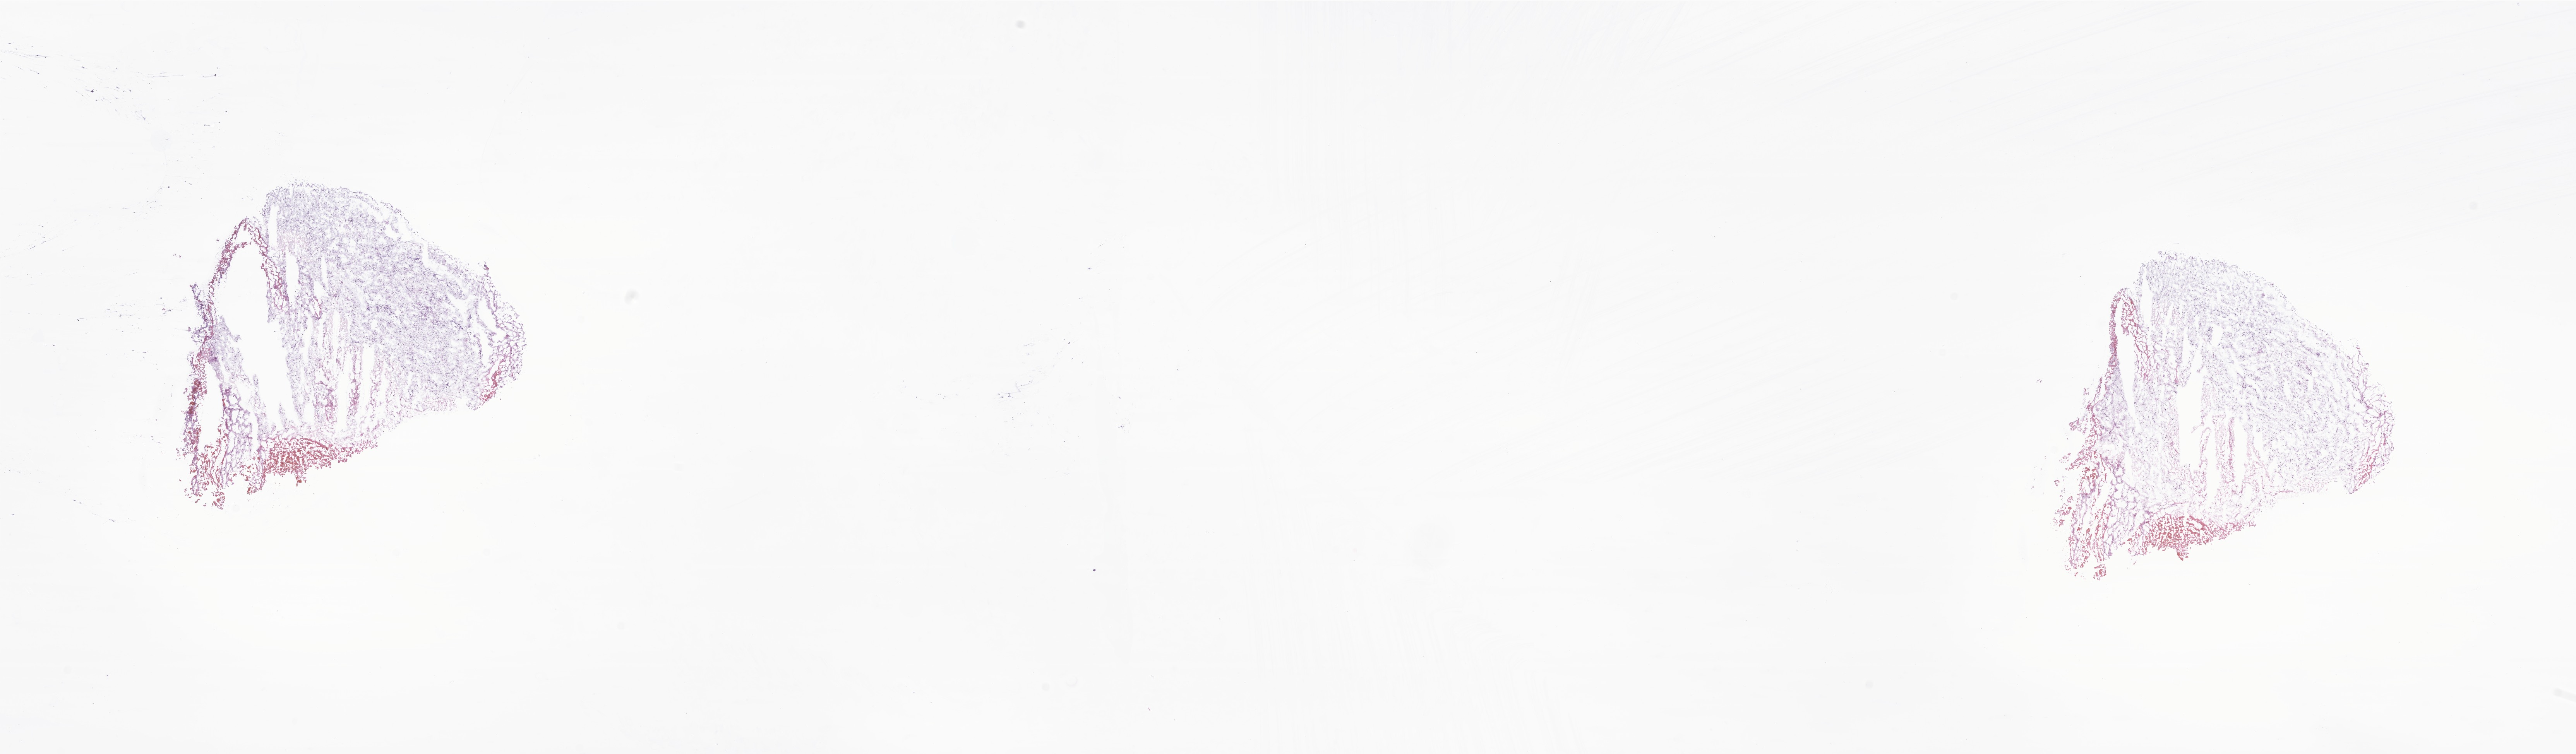
Digitized H&E-stained section of tumor tissue from the brain stem — whole scanned area (about 28.1 x 8.2 mm) shown as a low-resolution overview, cryosection (OCT / tissue freezing medium). Male patient, age 115 months (9 years 7 months).
Recorded diagnosis: Neoplasm, uncertain whether benign or malignant.